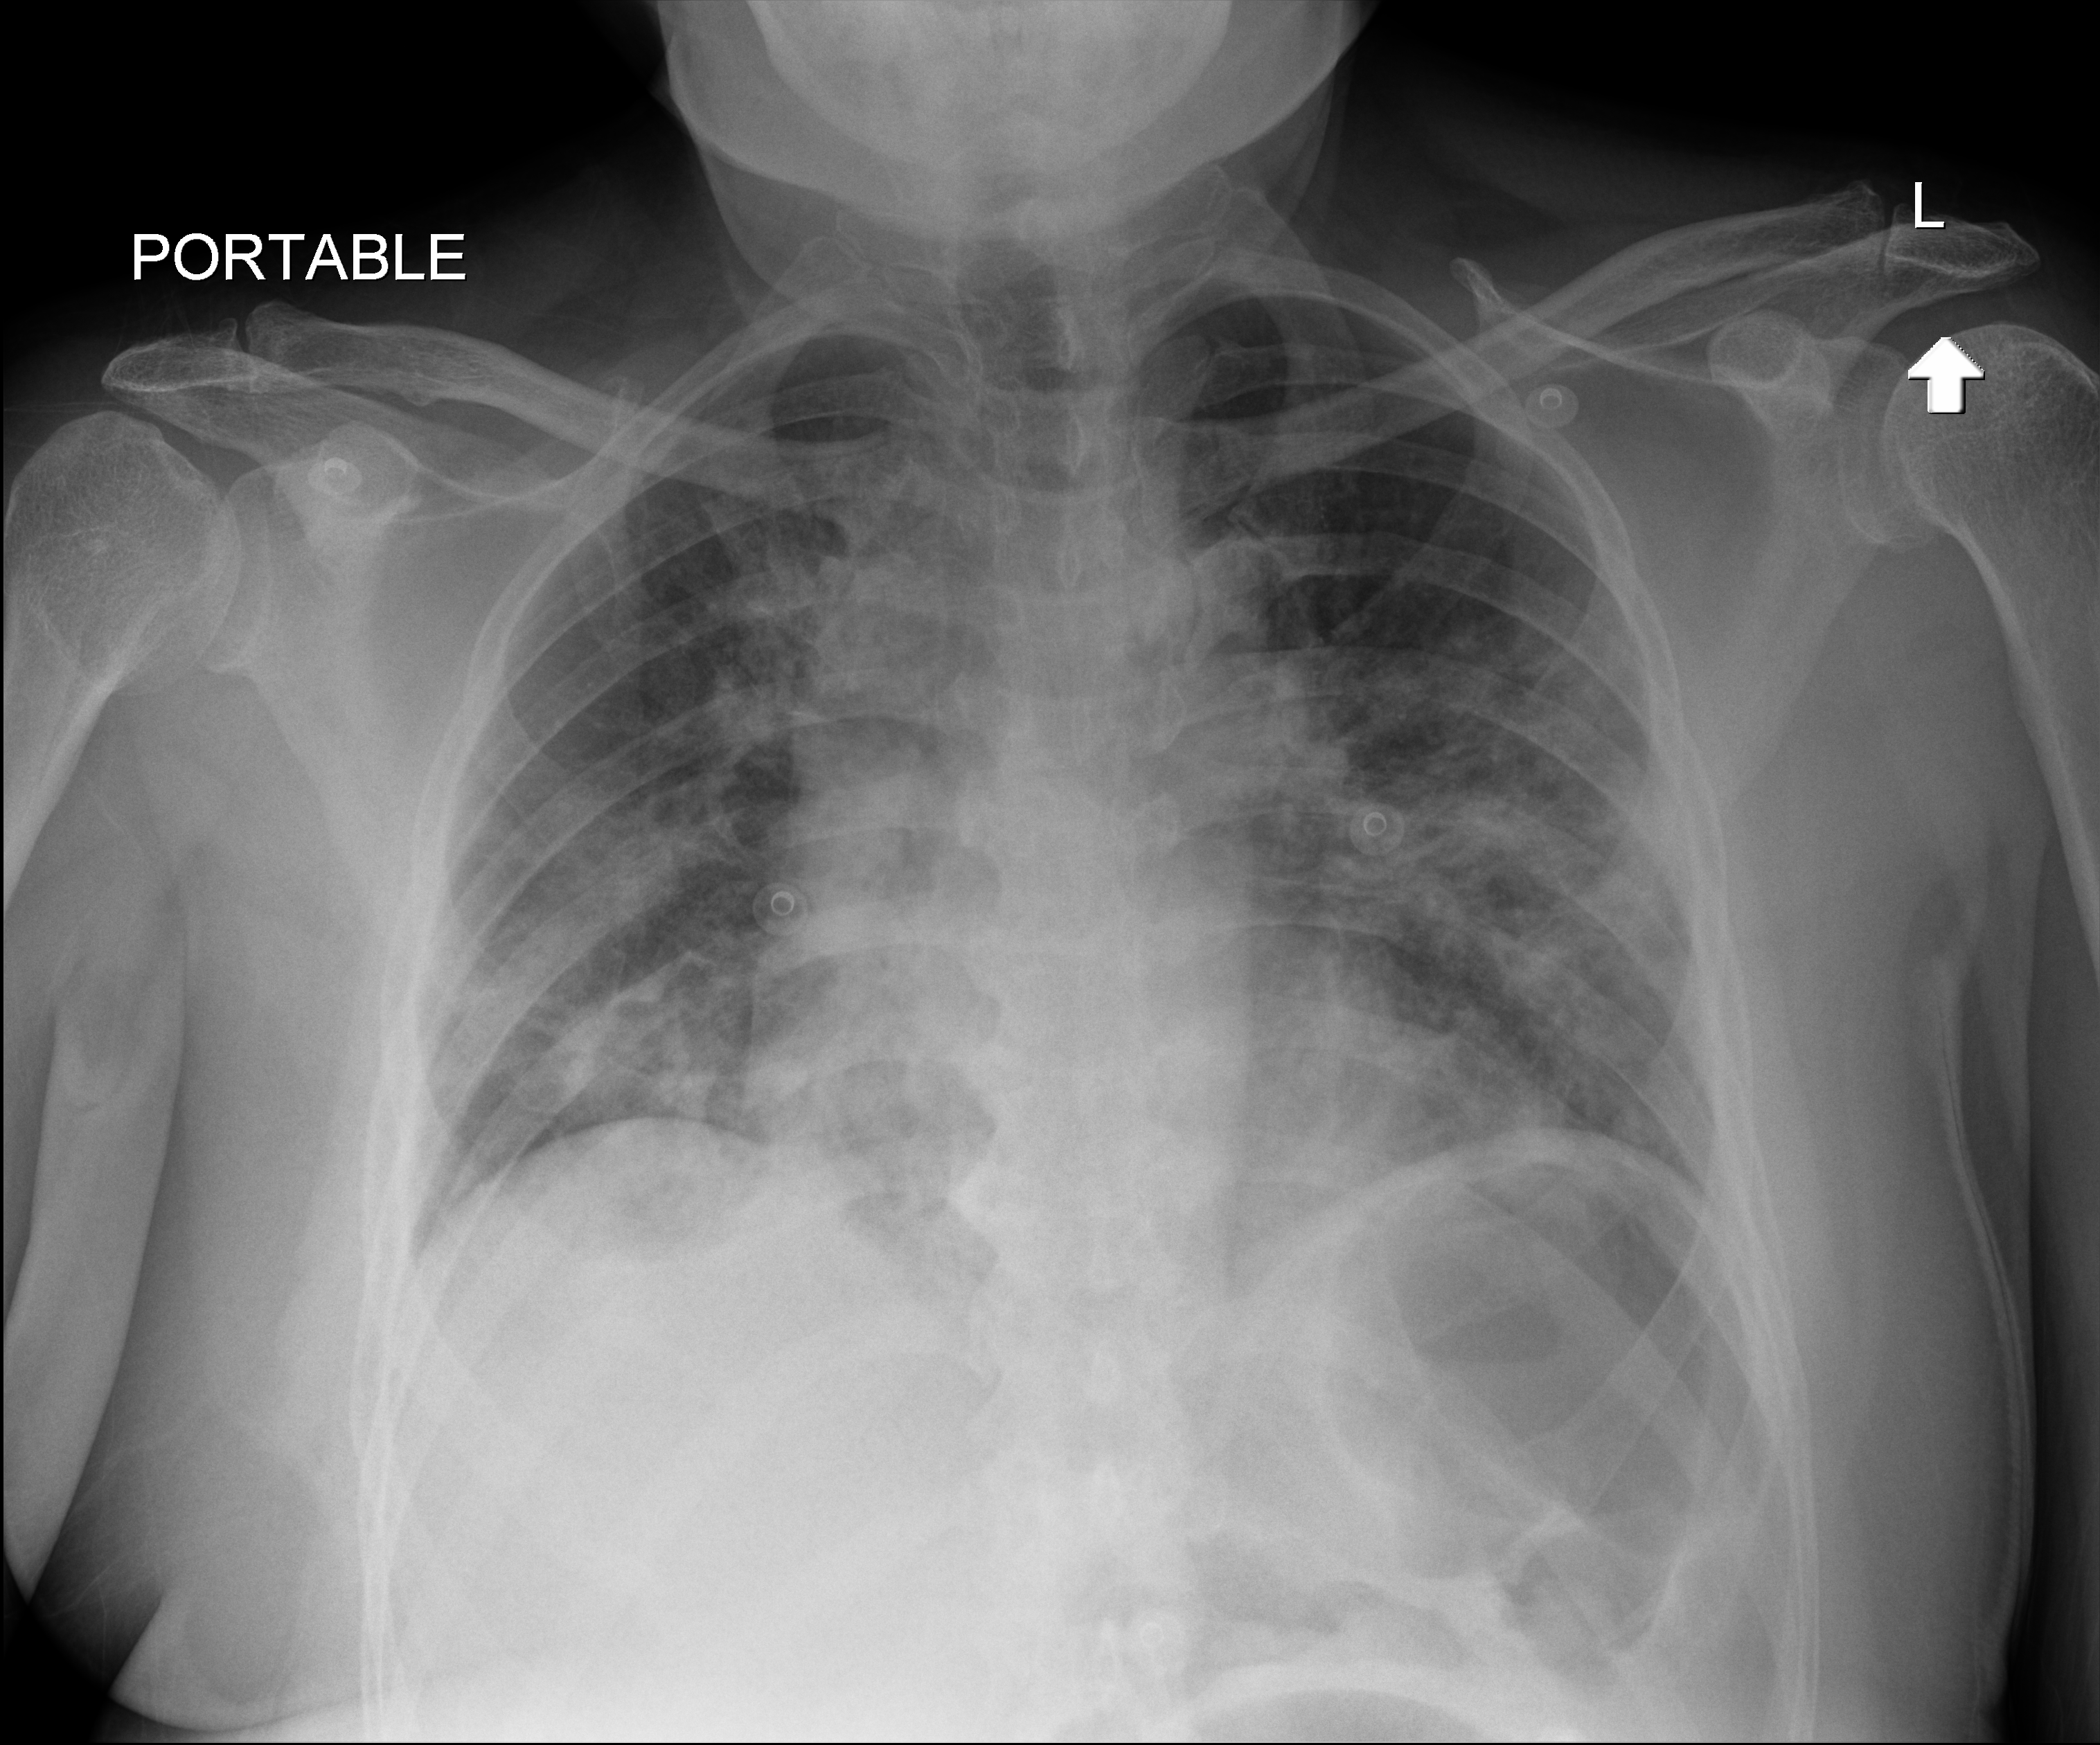
Chest X-ray, anteroposterior (AP) projection. Male patient hospitalised with COVID-19, age 18–59 years.
From the hospital-stay record, not from the radiograph (when in the stay this image was taken is not recorded): COPD (admission record): no; mechanically ventilated during this hospital stay: no.